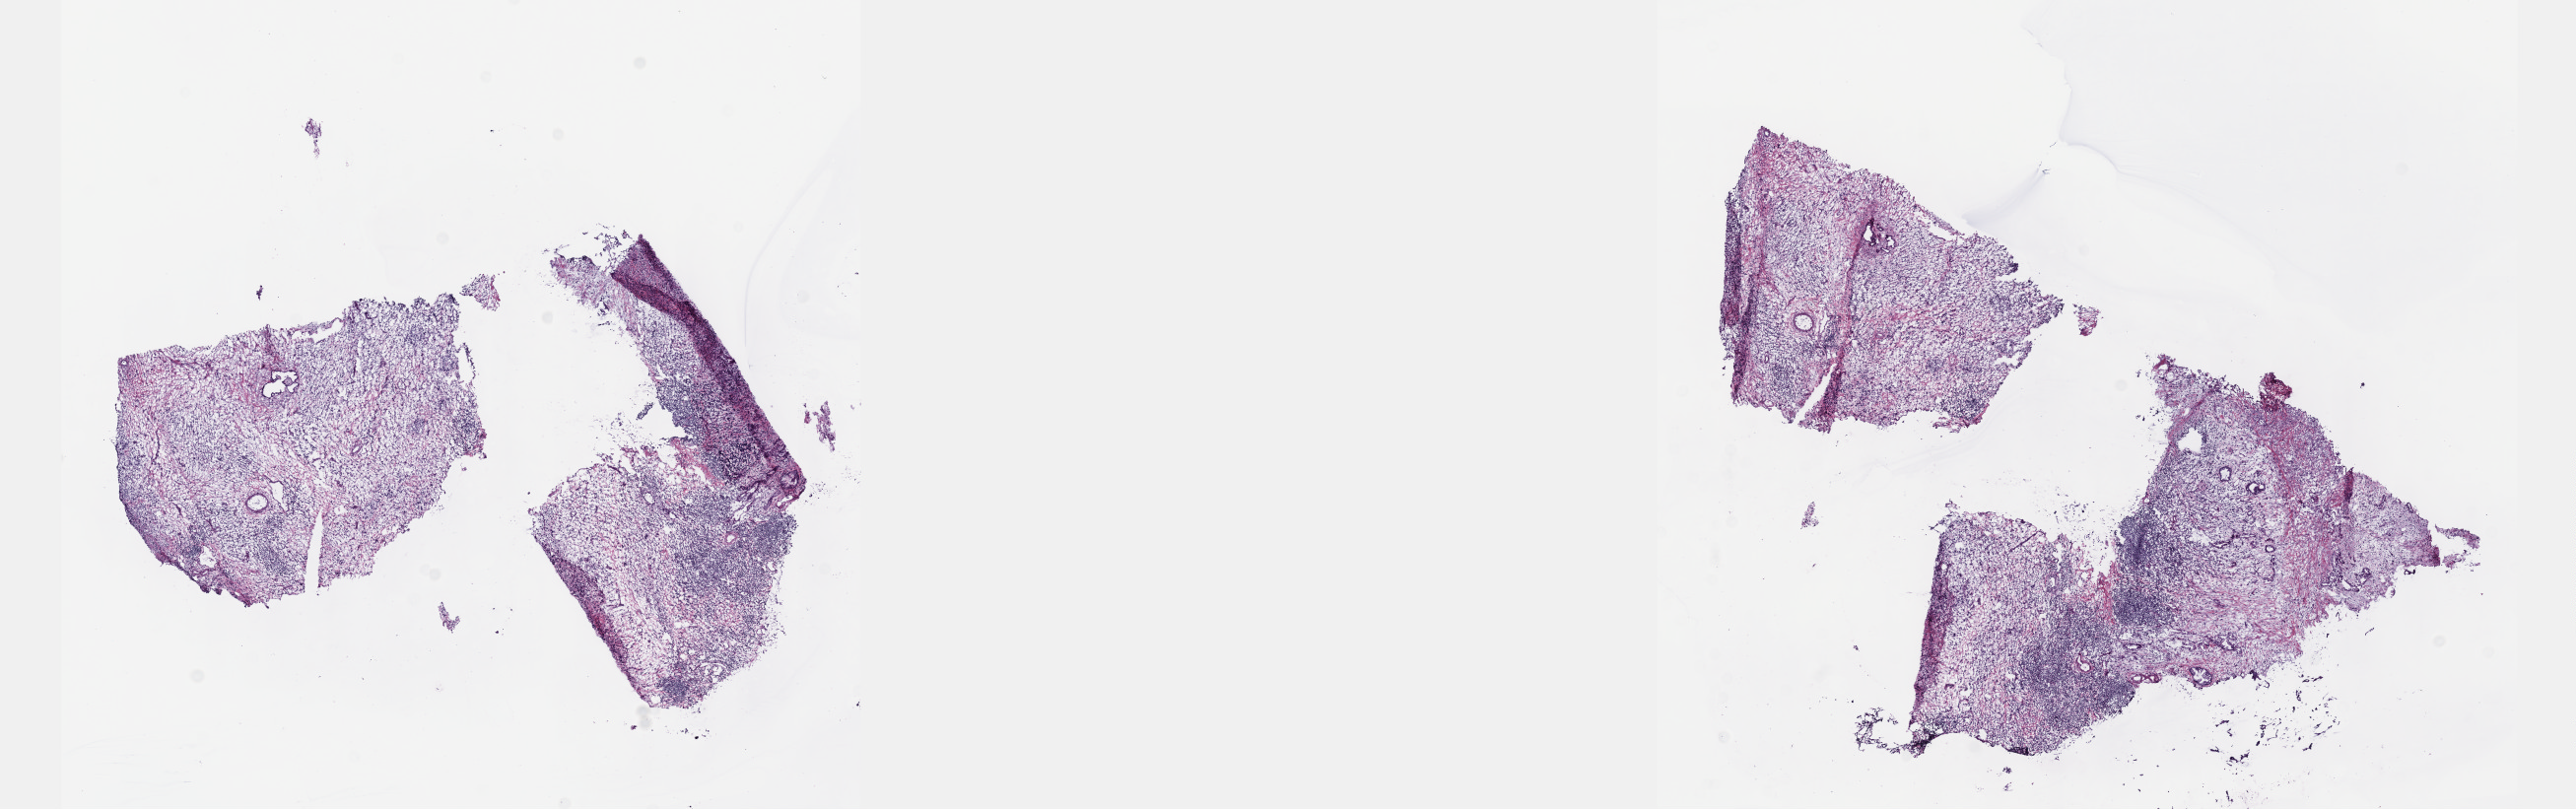
Digitized H&E tissue section (whole slide), a low-resolution overview of the entire scanned area, about 21.1 x 6.6 mm. Frozen section from the top of the tissue portion. Sample: primary tumour, pancreas. Patient: male, age at initial diagnosis 67 years. Histologic grade: G1 (well differentiated). Slide review estimates, as recorded: tumour cells 10%, tumour nuclei 10%, normal cells 20%, stromal cells 70%, necrosis 0%. Inflammatory infiltration, as recorded: lymphocyte infiltration 7%, monocyte infiltration 1%, neutrophil infiltration 9%.
Pathologic diagnosis: Infiltrating duct carcinoma, NOS (head of pancreas). AJCC pathologic stage: IIB (7th edition).